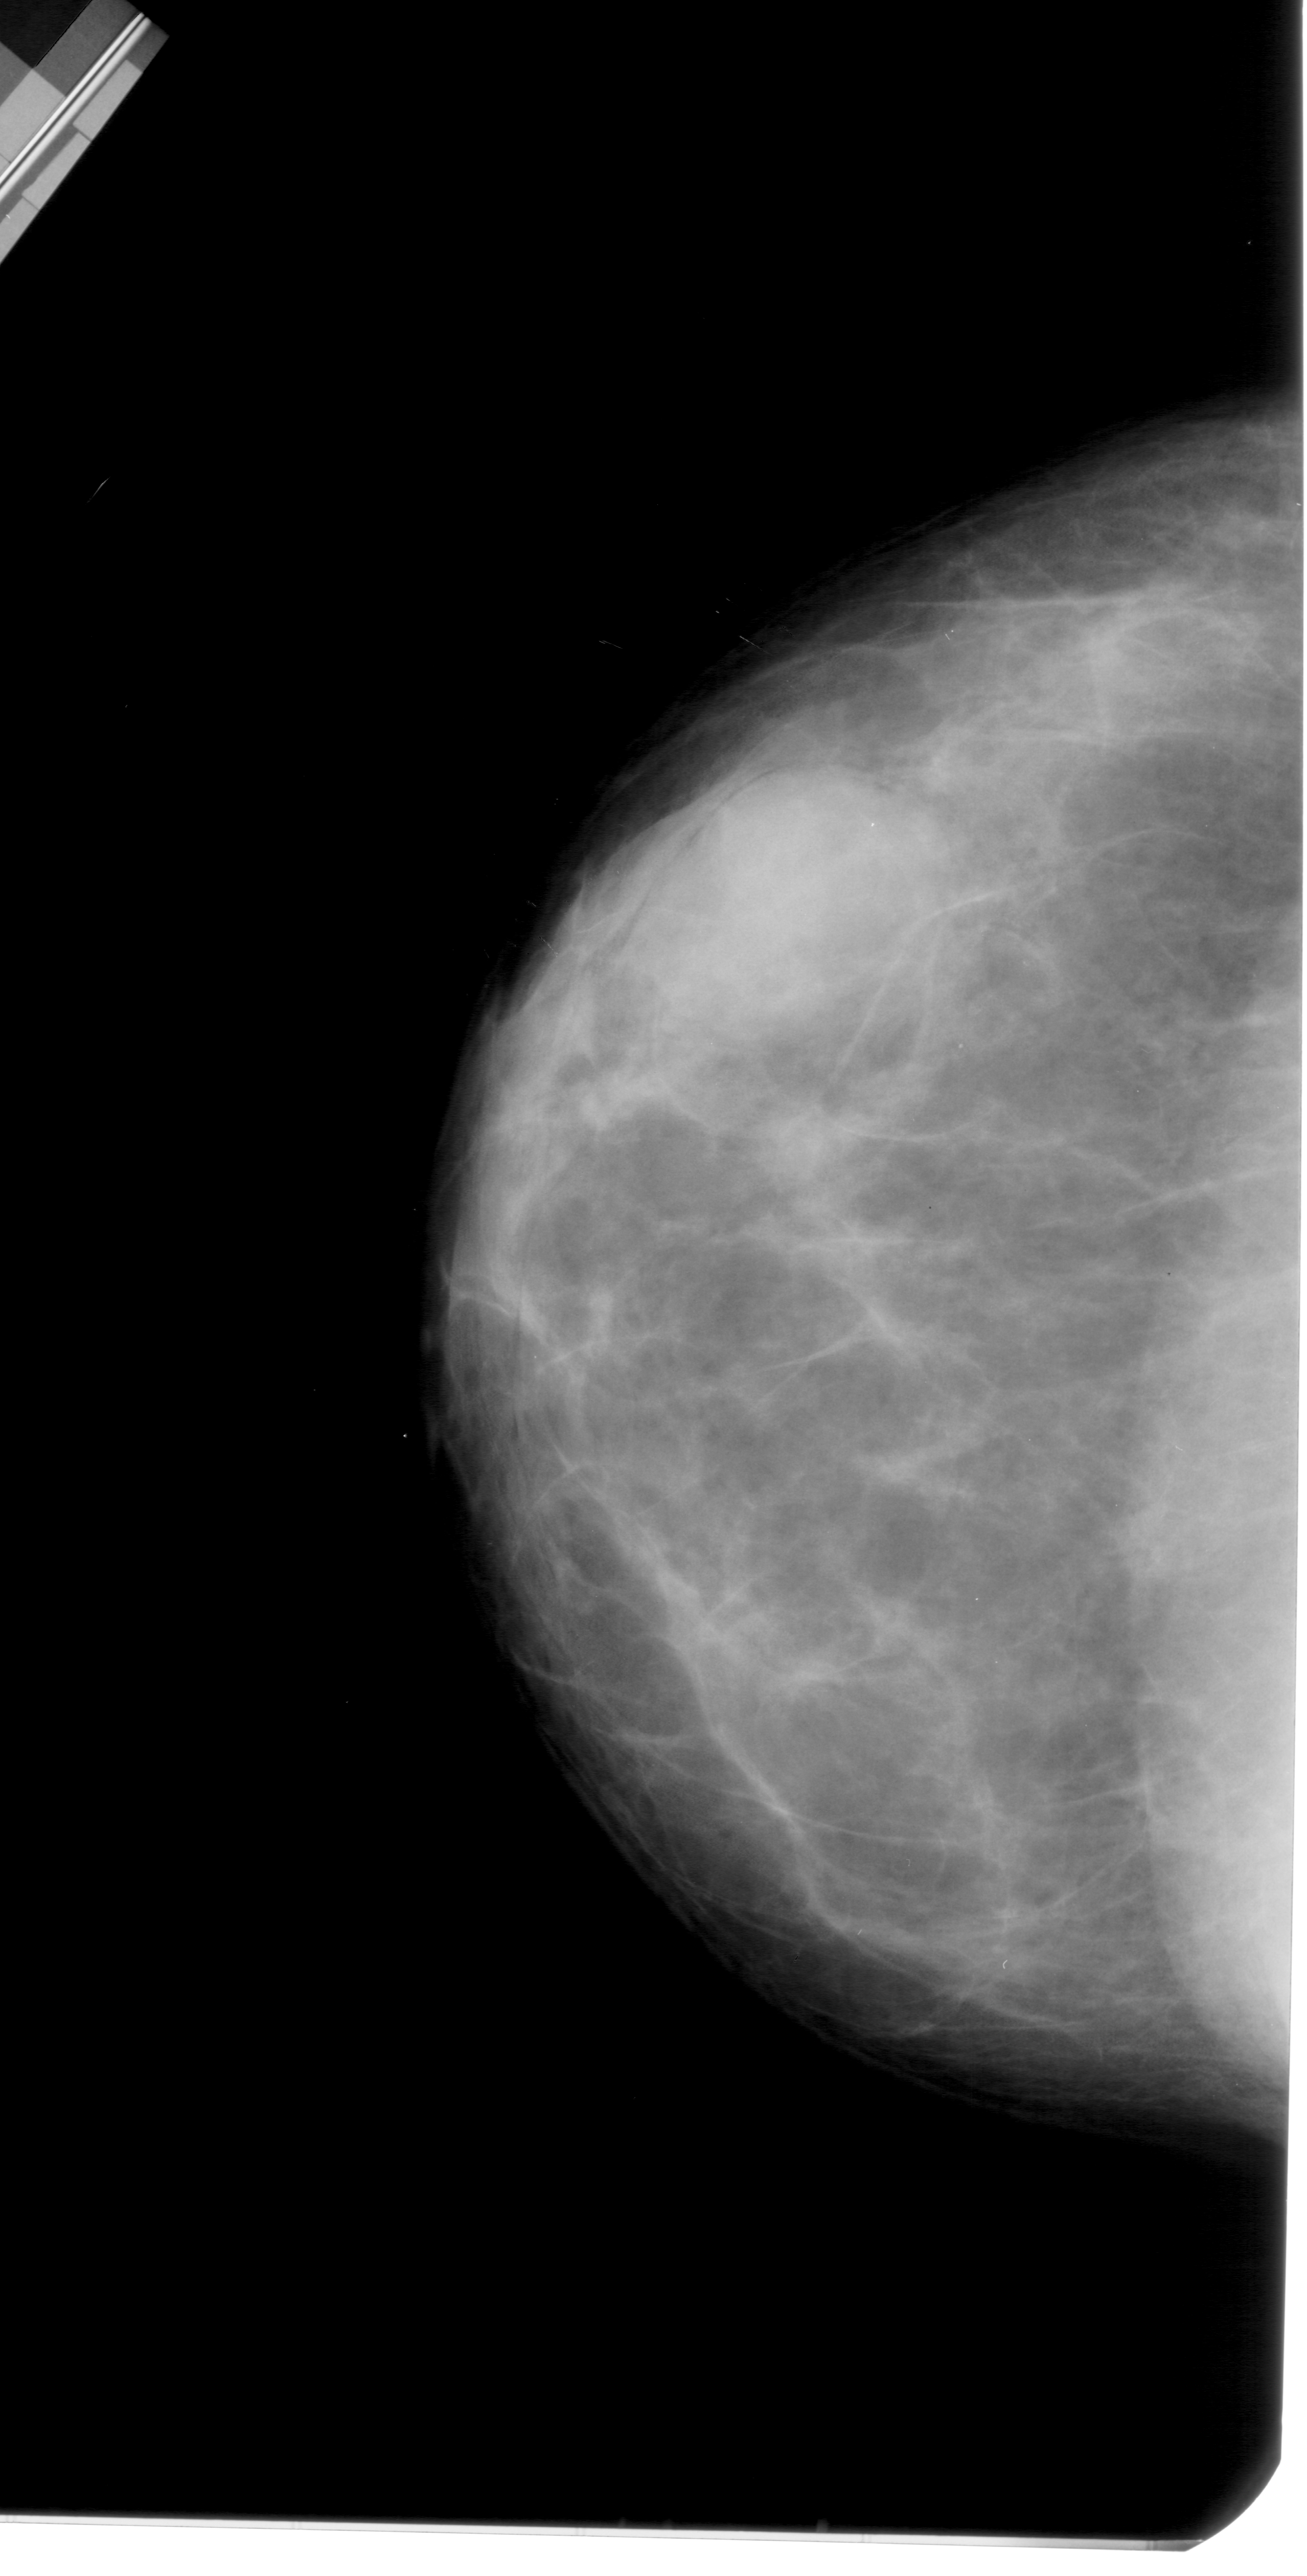
Scanned film-screen mammogram. Left breast. Craniocaudal (CC) view. Breast composition: extremely dense (BI-RADS density category 4 of 4). 1307 × 2576 image matrix.
Expert-marked regions of interest on this film, with their recorded descriptors:
- mass, shape oval, margins obscured; BI-RADS assessment category 4; subtlety rating 4 on a 1 (subtle) to 5 (obvious) scale; pathology result (as recorded, not read from the image): benign: bounding box <683,767,890,995> (left, top, right, bottom; pixels)